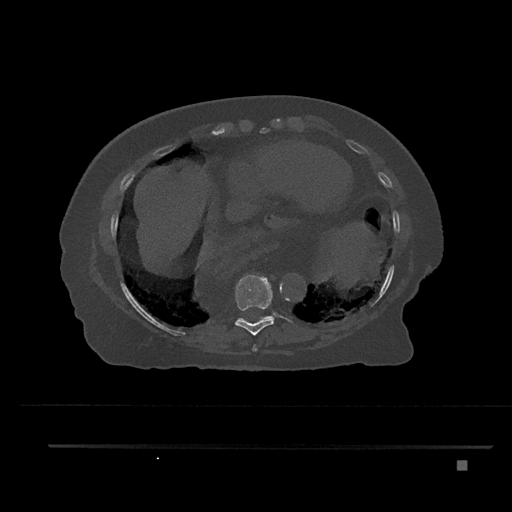
CT including the spine, one axial slice; position 393 of 797 along the scan axis; reconstruction kernel Br40s/3; 120 kVp; bone window (W 1800 / L 400 HU); 512 × 512 image matrix, field of view 437 × 437 mm. Female patient, age 76 years. From the clinical record (not read from this slice): primary cancer: lung; vertebrae with lytic lesions (as recorded): T11, L3.
Annotated regions visible in this slice (semi-automatically segmented with operator editing):
- T10 vertebra: bounding box (x1, y1, x2, y2) in pixels: (260, 317, 264, 320)
- T8 vertebra: (252, 344, 257, 352)
- T9 vertebra: (235, 275, 274, 336)